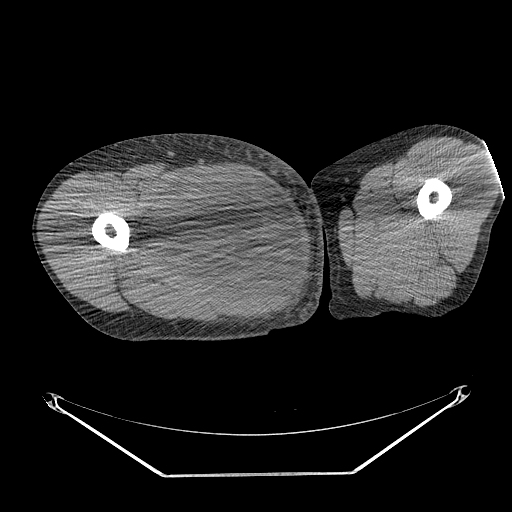
CT of an extremity soft-tissue mass (from a PET/CT study), one axial slice; position 255 of 311 along the scan axis; 140 kVp; soft-tissue window (W 400 / L 40 HU); 512 × 512 image matrix, field of view 500 × 500 mm. Male patient. Case-level facts recorded for this patient, not image findings: histological type: undifferentiated - pleiomorphic; grade: high; site of the primary tumour: right thigh.
Structures marked on this image (expert contour drawn on MRI and transferred to this co-registered scan by the dataset authors):
- gross tumour volume including surrounding oedema: bounding box (x1, y1, x2, y2) in pixels: (139, 169, 264, 273)
- gross tumour volume (mass): (153, 171, 263, 268)